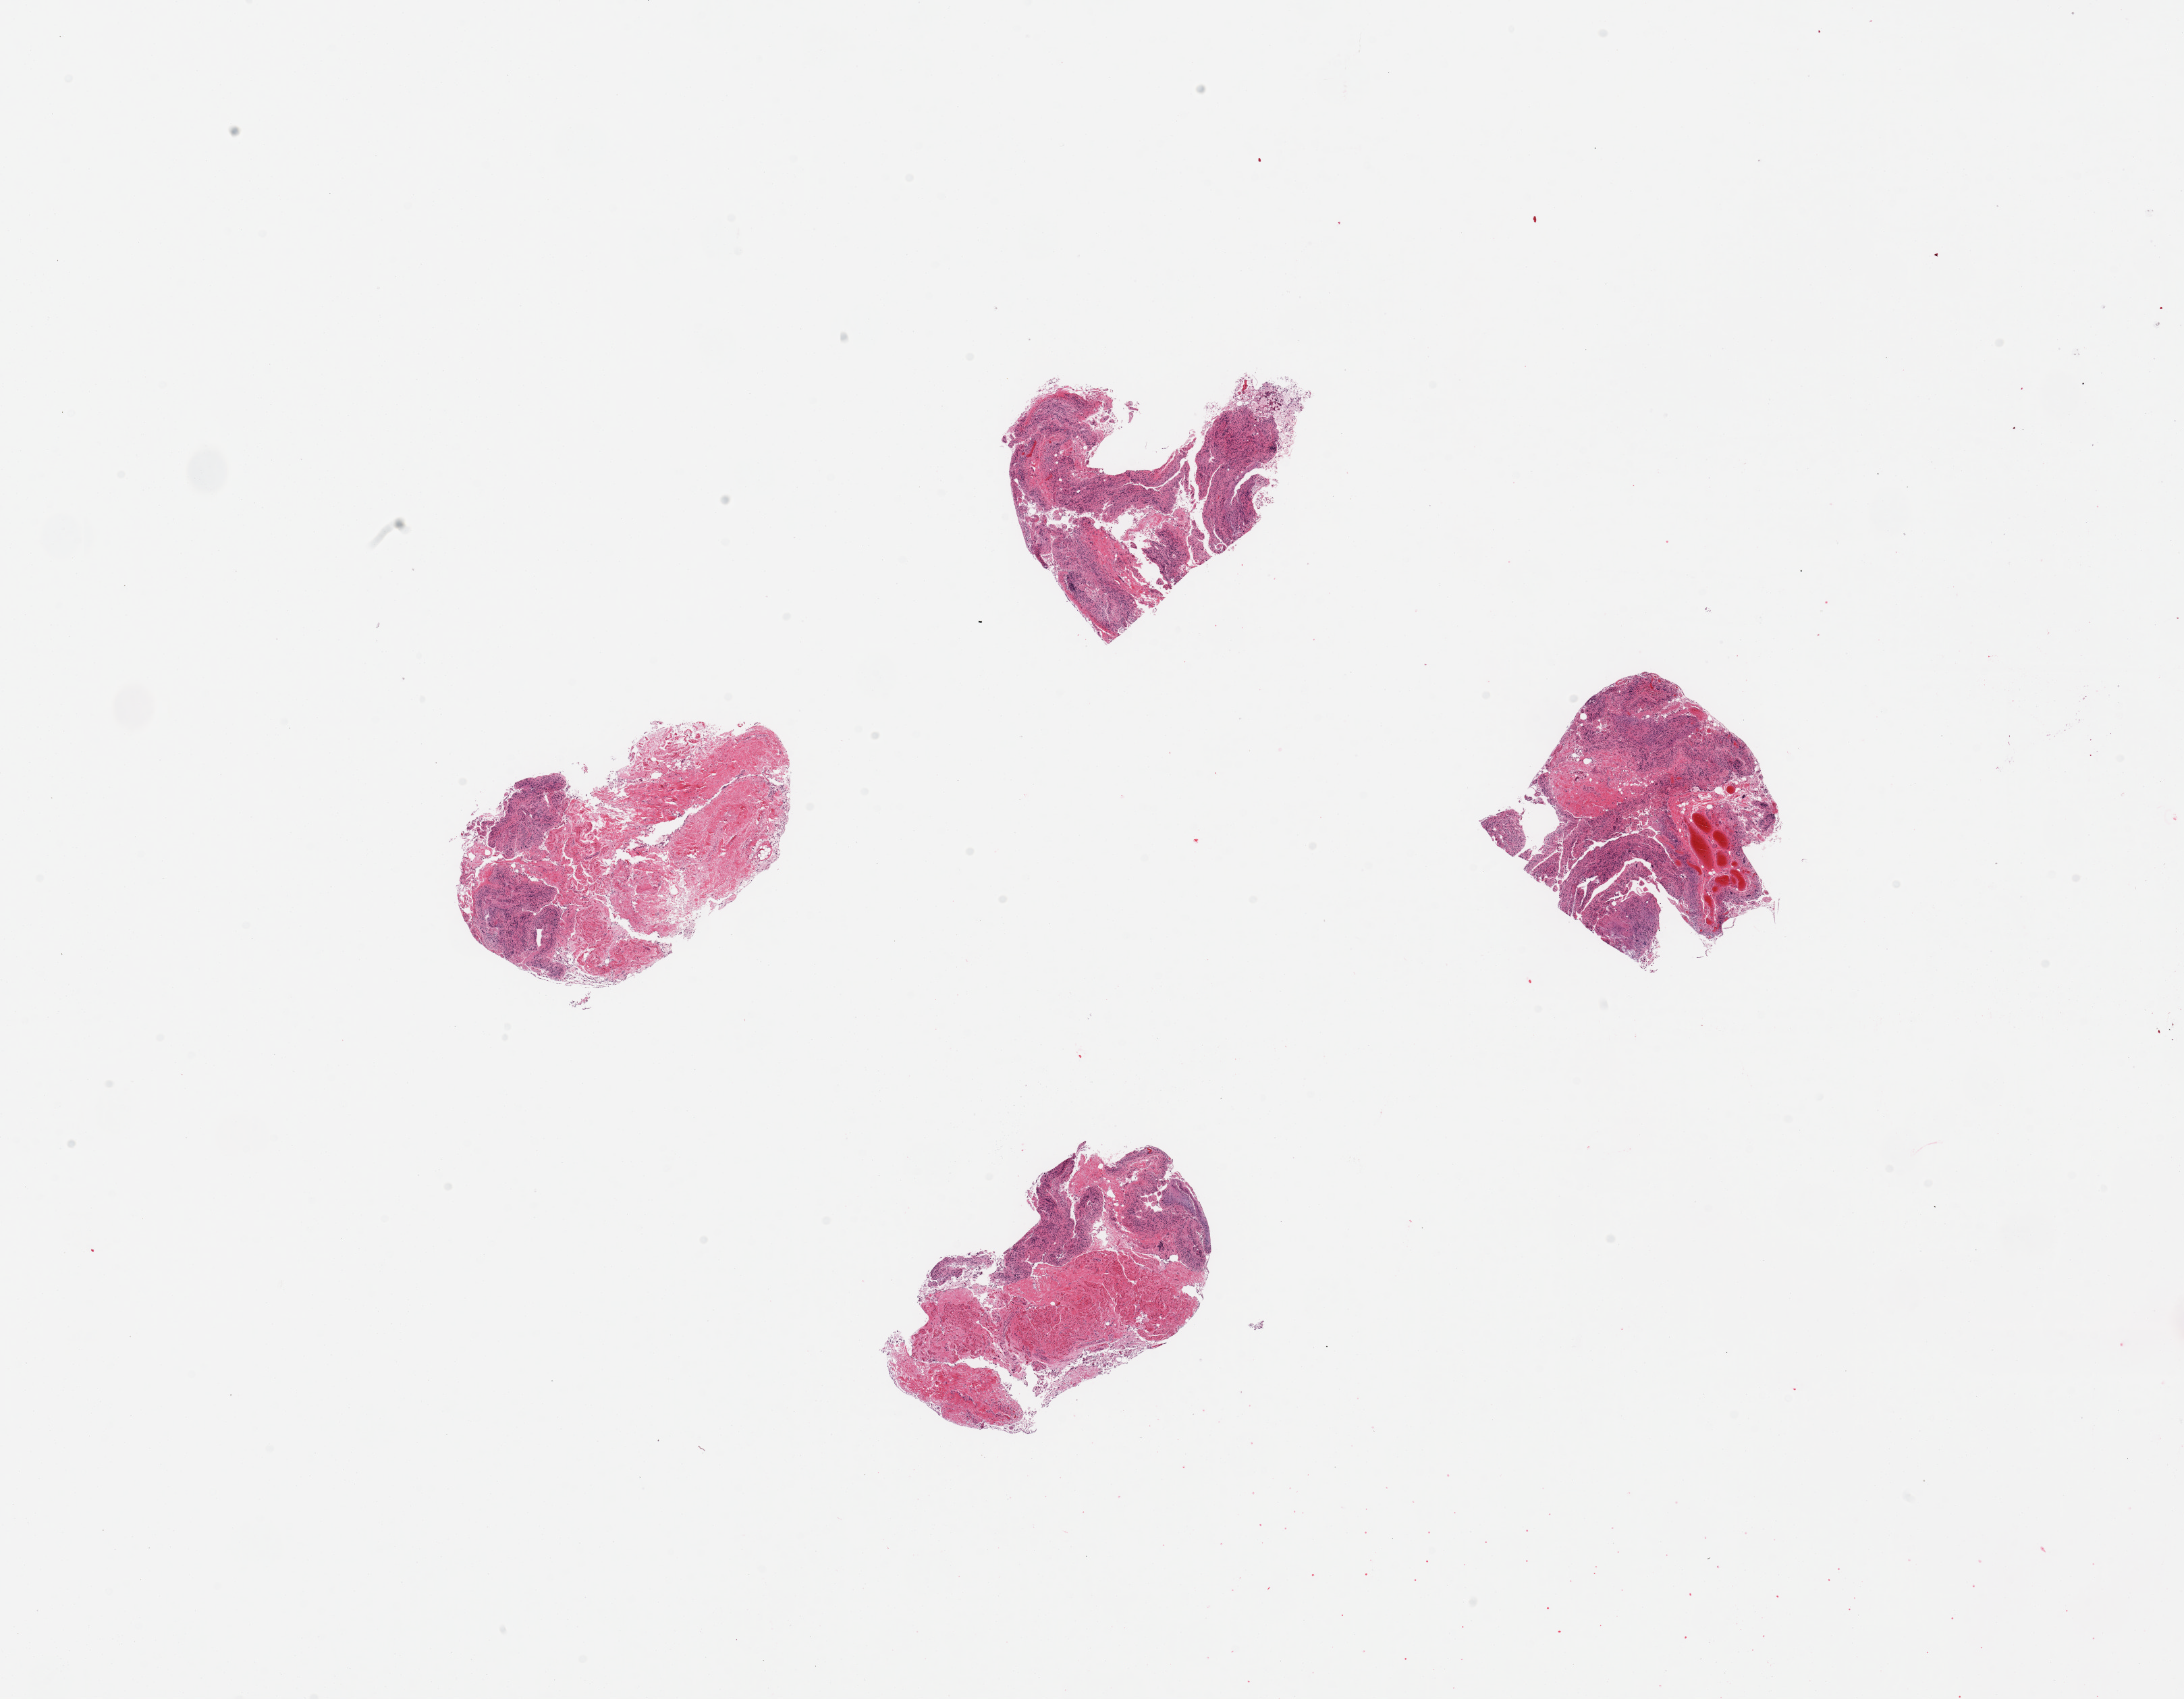
Digitized hematoxylin and eosin (H&E)-stained section — whole scanned area (about 25.6 x 19.9 mm) shown as a low-resolution overview; PAXgene-fixed paraffin-embedded (PFPE) section; section of ileum (target tissue); tissue donor sample. Donor: male.
• reviewer comment on this tissue sample: 4 pieces; autolyzed with lack of target lymphoid aggregates